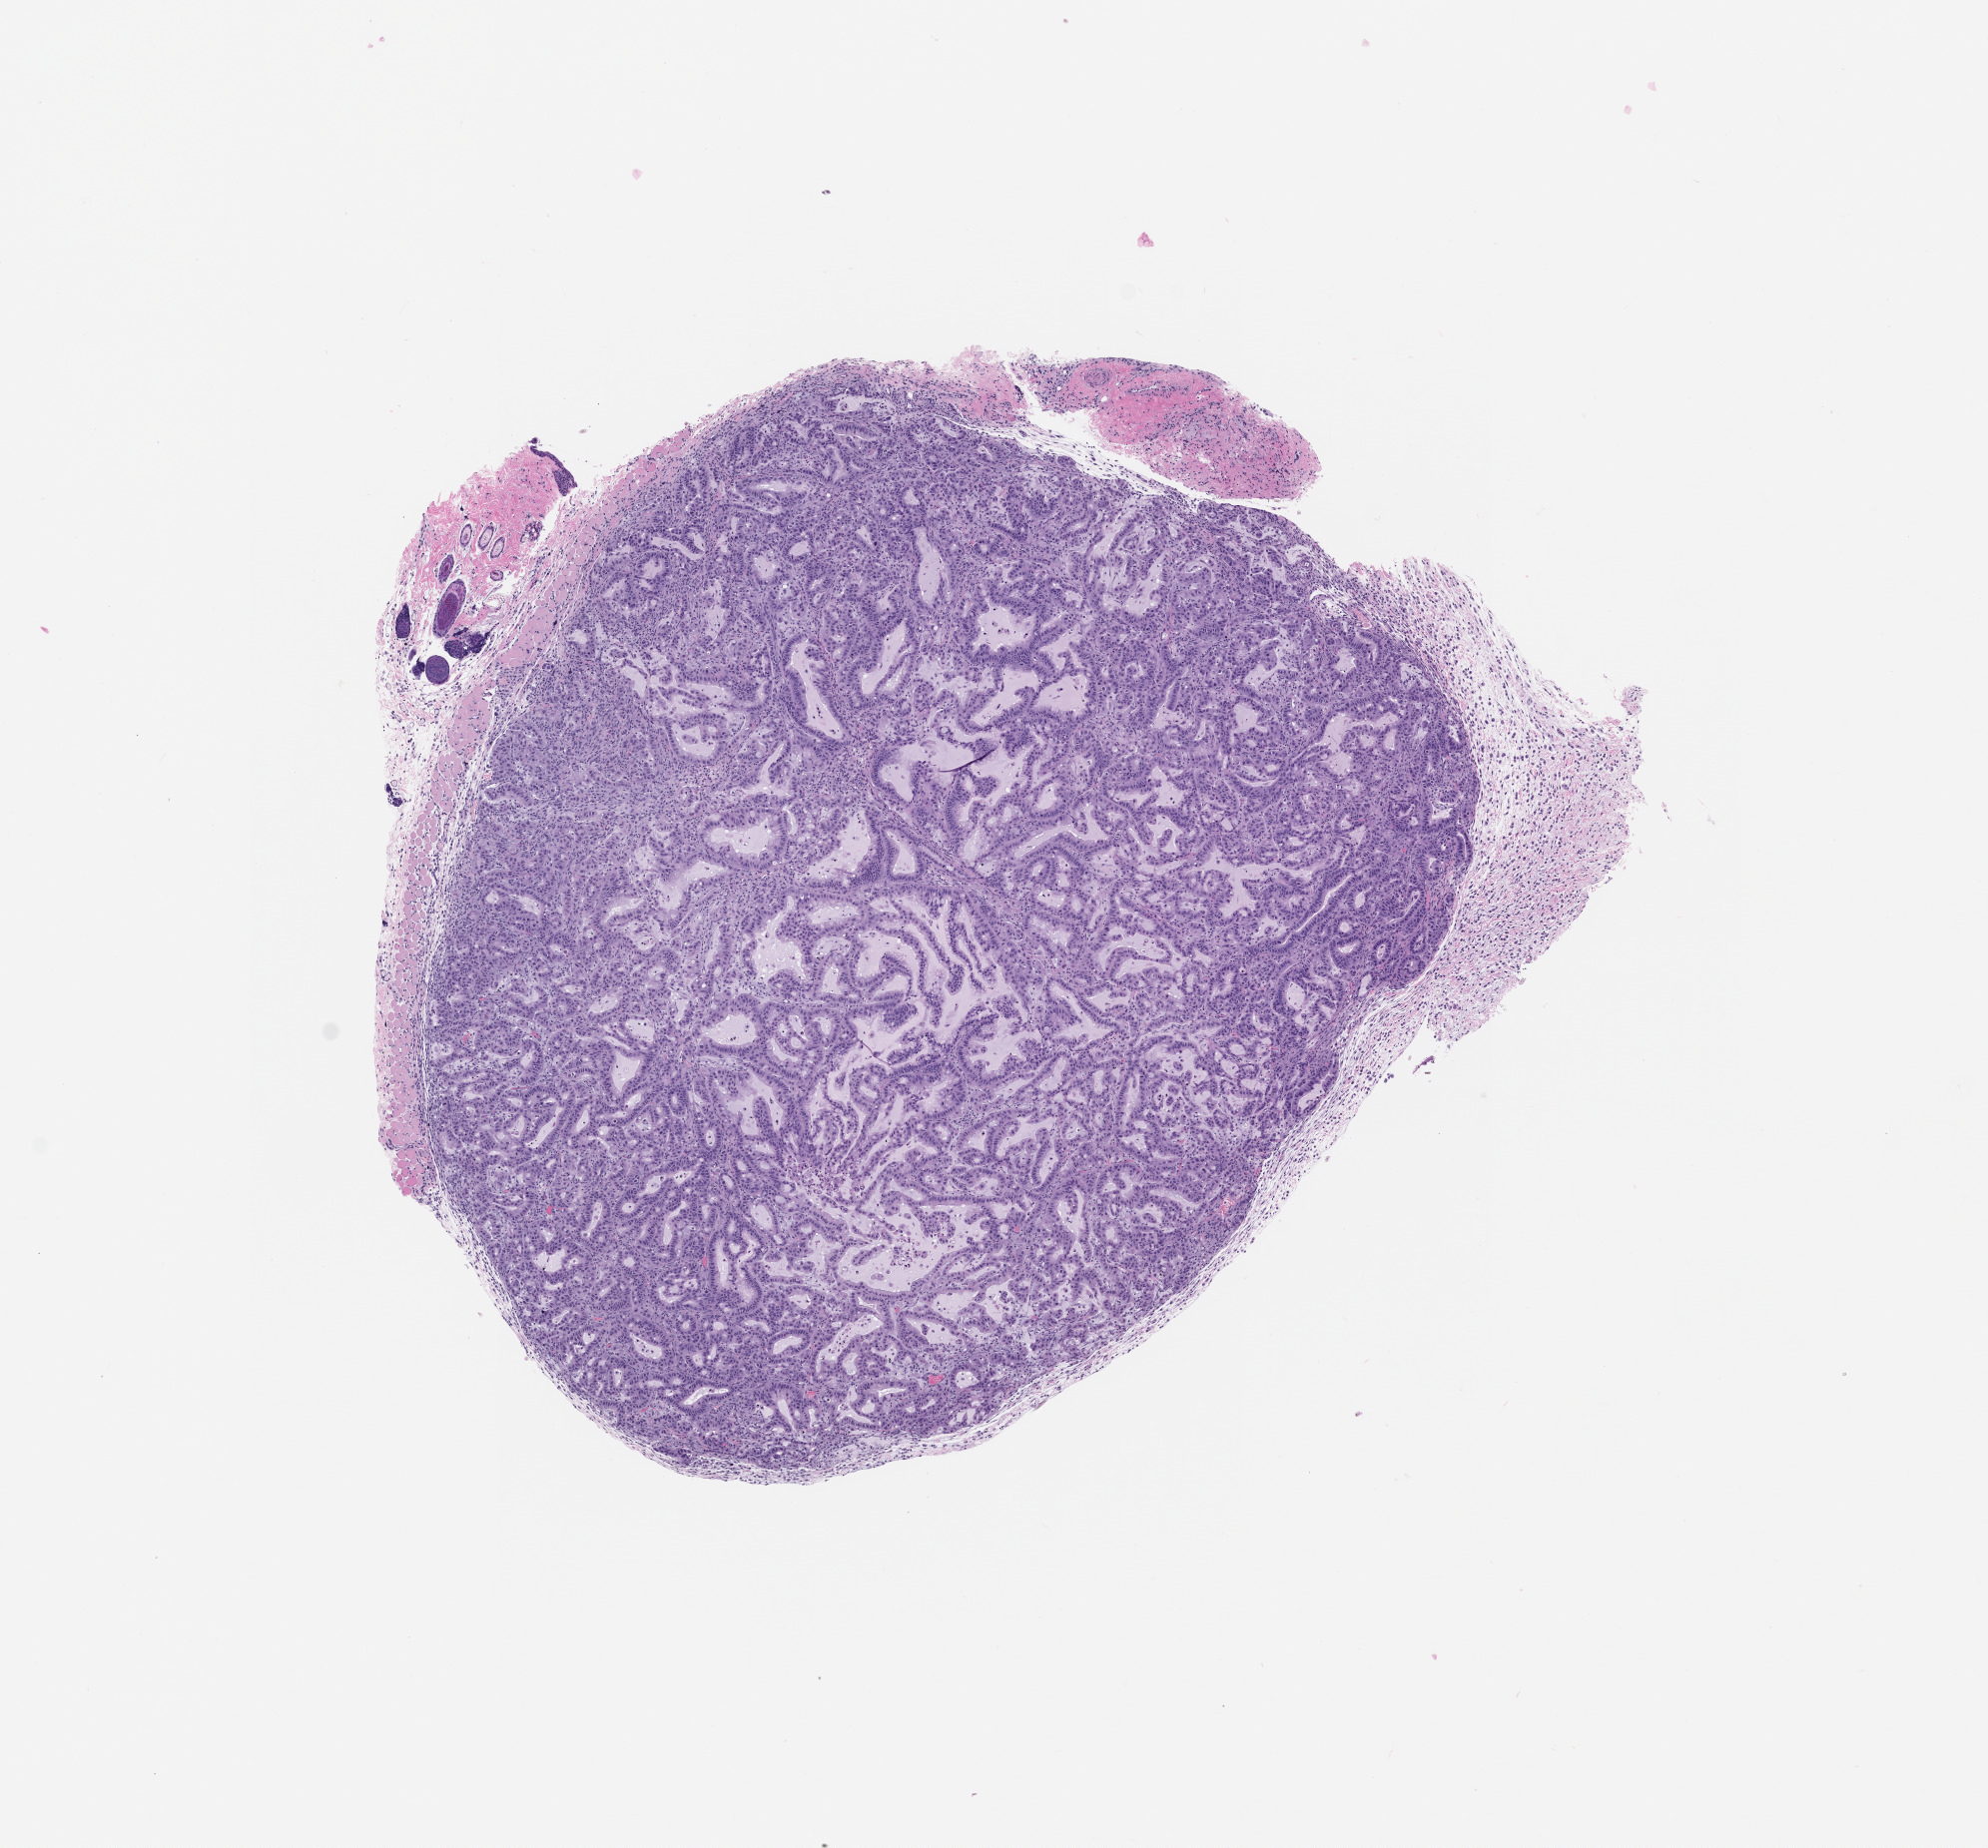
Whole-slide image, hematoxylin and eosin (H&E): patient-derived xenograft (human tumor grown in a mouse), passage 0 — low-resolution overview of the scanned area, about 8.0 x 7.4 mm, formalin-fixed, paraffin-embedded (FFPE) tissue, originating tumor site category: pancreas.
* originating patient diagnosis: Pancreatic Adenocarcinoma